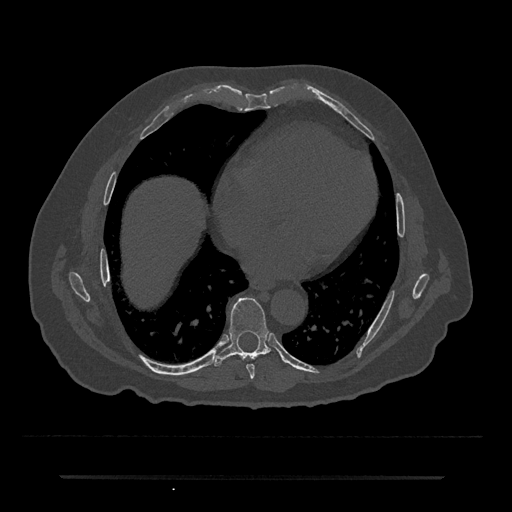
CT including the spine, one axial slice. Slice 347 of 797 in the series (ordered by position). Reconstruction kernel Br40s/3. 120 kVp. Bone window (W 1800 / L 400 HU). 0.5 mm slice thickness. 512 × 512 image matrix, field of view 437 × 437 mm. Male patient, age 69 years. From the clinical record (not read from this slice): primary cancer: prostate.
Outlined on this slice (semi-automatic segmentation, software-assisted and operator-edited):
- T7 vertebra: bounding box [x1, y1, x2, y2] px = [246, 364, 255, 379]
- T8 vertebra: [213, 298, 273, 366]